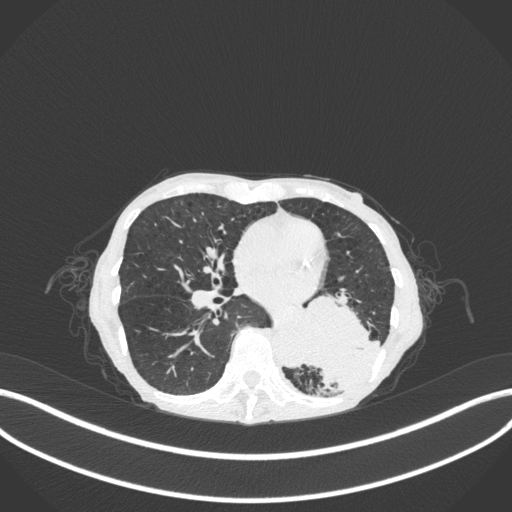
Chest CT, one axial slice. Slice 125 of 347 in the series (ordered by position). Reconstruction kernel B31f. Lung window (W 1500 / L -600 HU). 1 mm slice thickness. 512 × 512 image matrix. Female patient, age 70 years. Case-level facts recorded for this patient, not image findings: clinical TNM (as recorded): T3 N0 M0.
Outlined on this slice (bounding box drawn by a radiologist):
- lung tumour (recorded histology: small cell carcinoma): box from (x=294, y=286) to (x=385, y=389) px